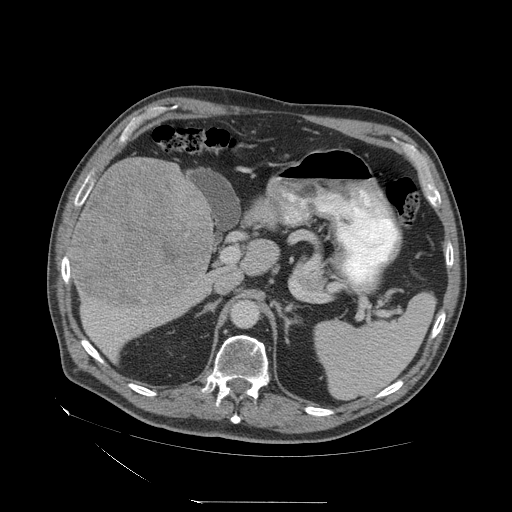
Contrast-enhanced abdominal CT (liver protocol), one axial slice; position 29 of 83 along the scan axis; reconstruction kernel STANDARD; 140 kVp; soft-tissue window (W 400 / L 40 HU); 2.5 mm slice thickness; 512 × 512 image matrix, field of view 460 × 460 mm. Case-level facts recorded for this patient, not image findings: diagnosis: hepatocellular carcinoma (patient treated with transarterial chemoembolisation; whether this scan precedes or follows treatment is not stated here); TNM stage (as recorded): Stage-I; Child-Pugh class: A; tumour differentiation: well differentiated.
Outlined on this slice (semi-automatically segmented with operator editing):
- liver parenchyma outside the tumour (the mass and vessels are separate outlines, so this box may not span the whole liver): bounding box (x1, y1, x2, y2) in pixels: (68, 156, 214, 360)
- mass: (71, 158, 211, 307)